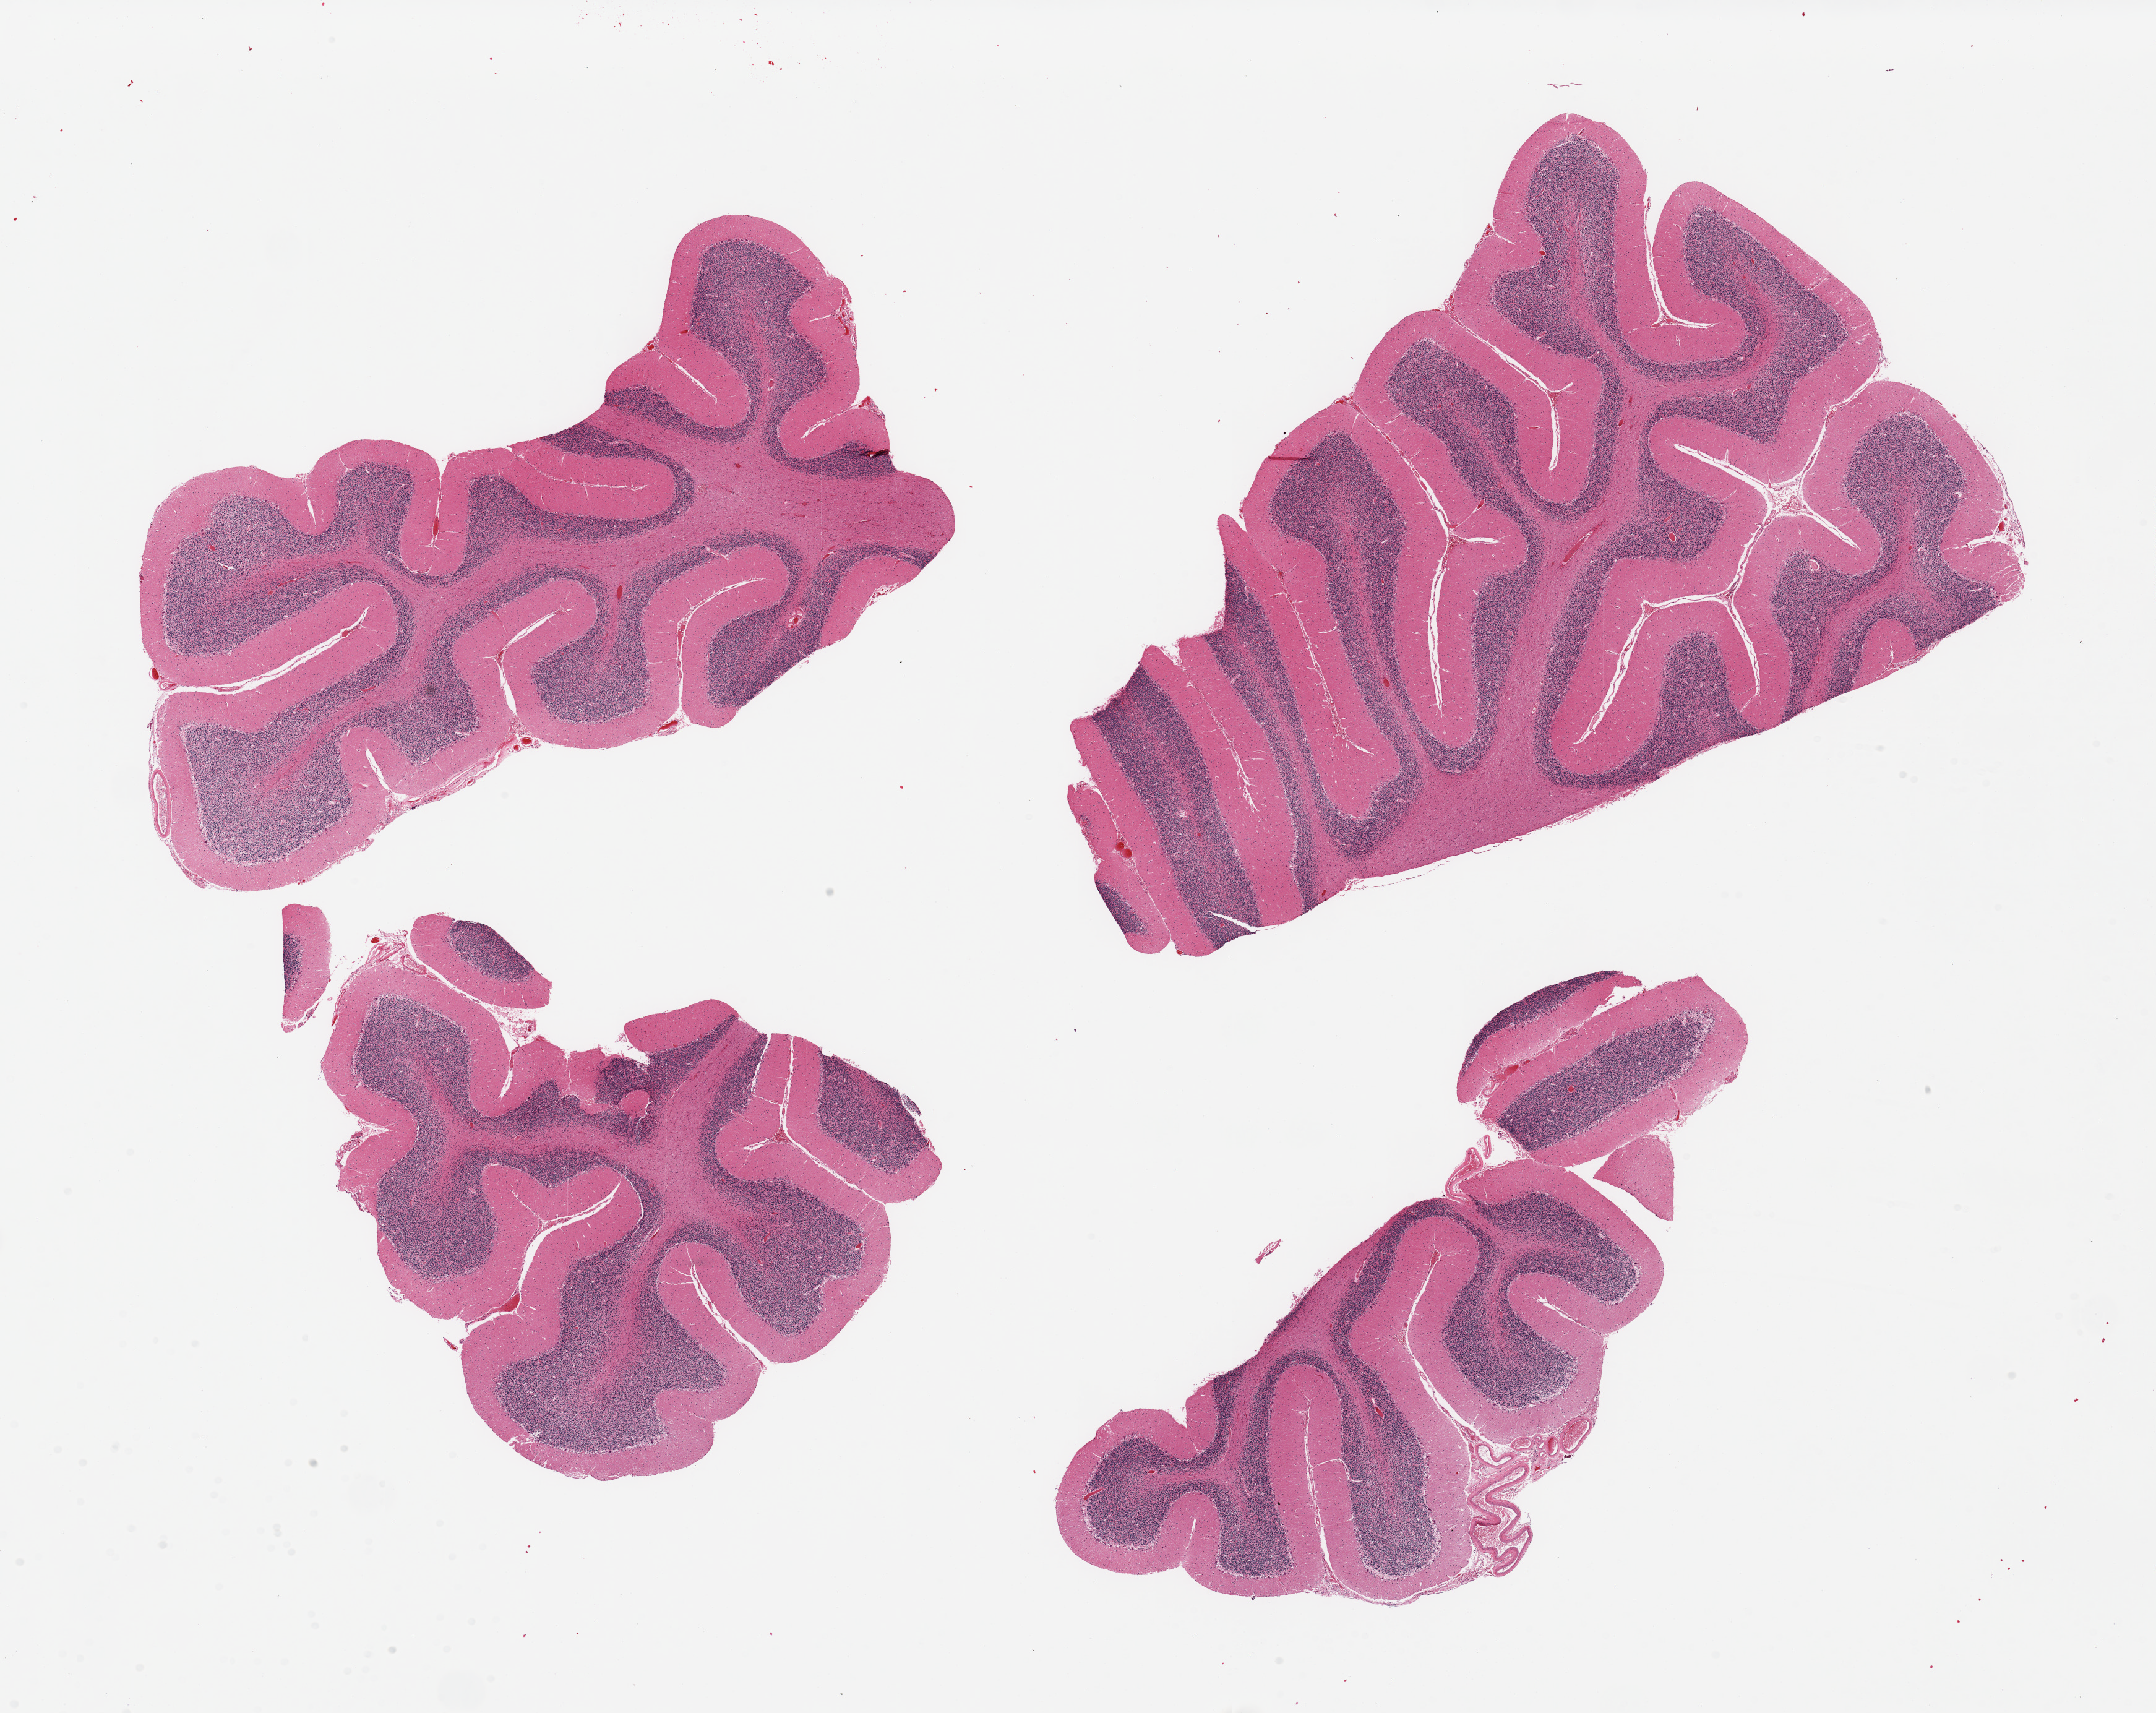
Whole-slide image, haematoxylin and eosin stain — low-resolution overview of the scanned area, about 27.6 x 21.9 mm, PAXgene-fixed paraffin-embedded (PFPE) section, section of cerebellum (target tissue), tissue donor sample. Donor: male.
• review note (as recorded): 4 pieces; focus of meningeal blood vessels